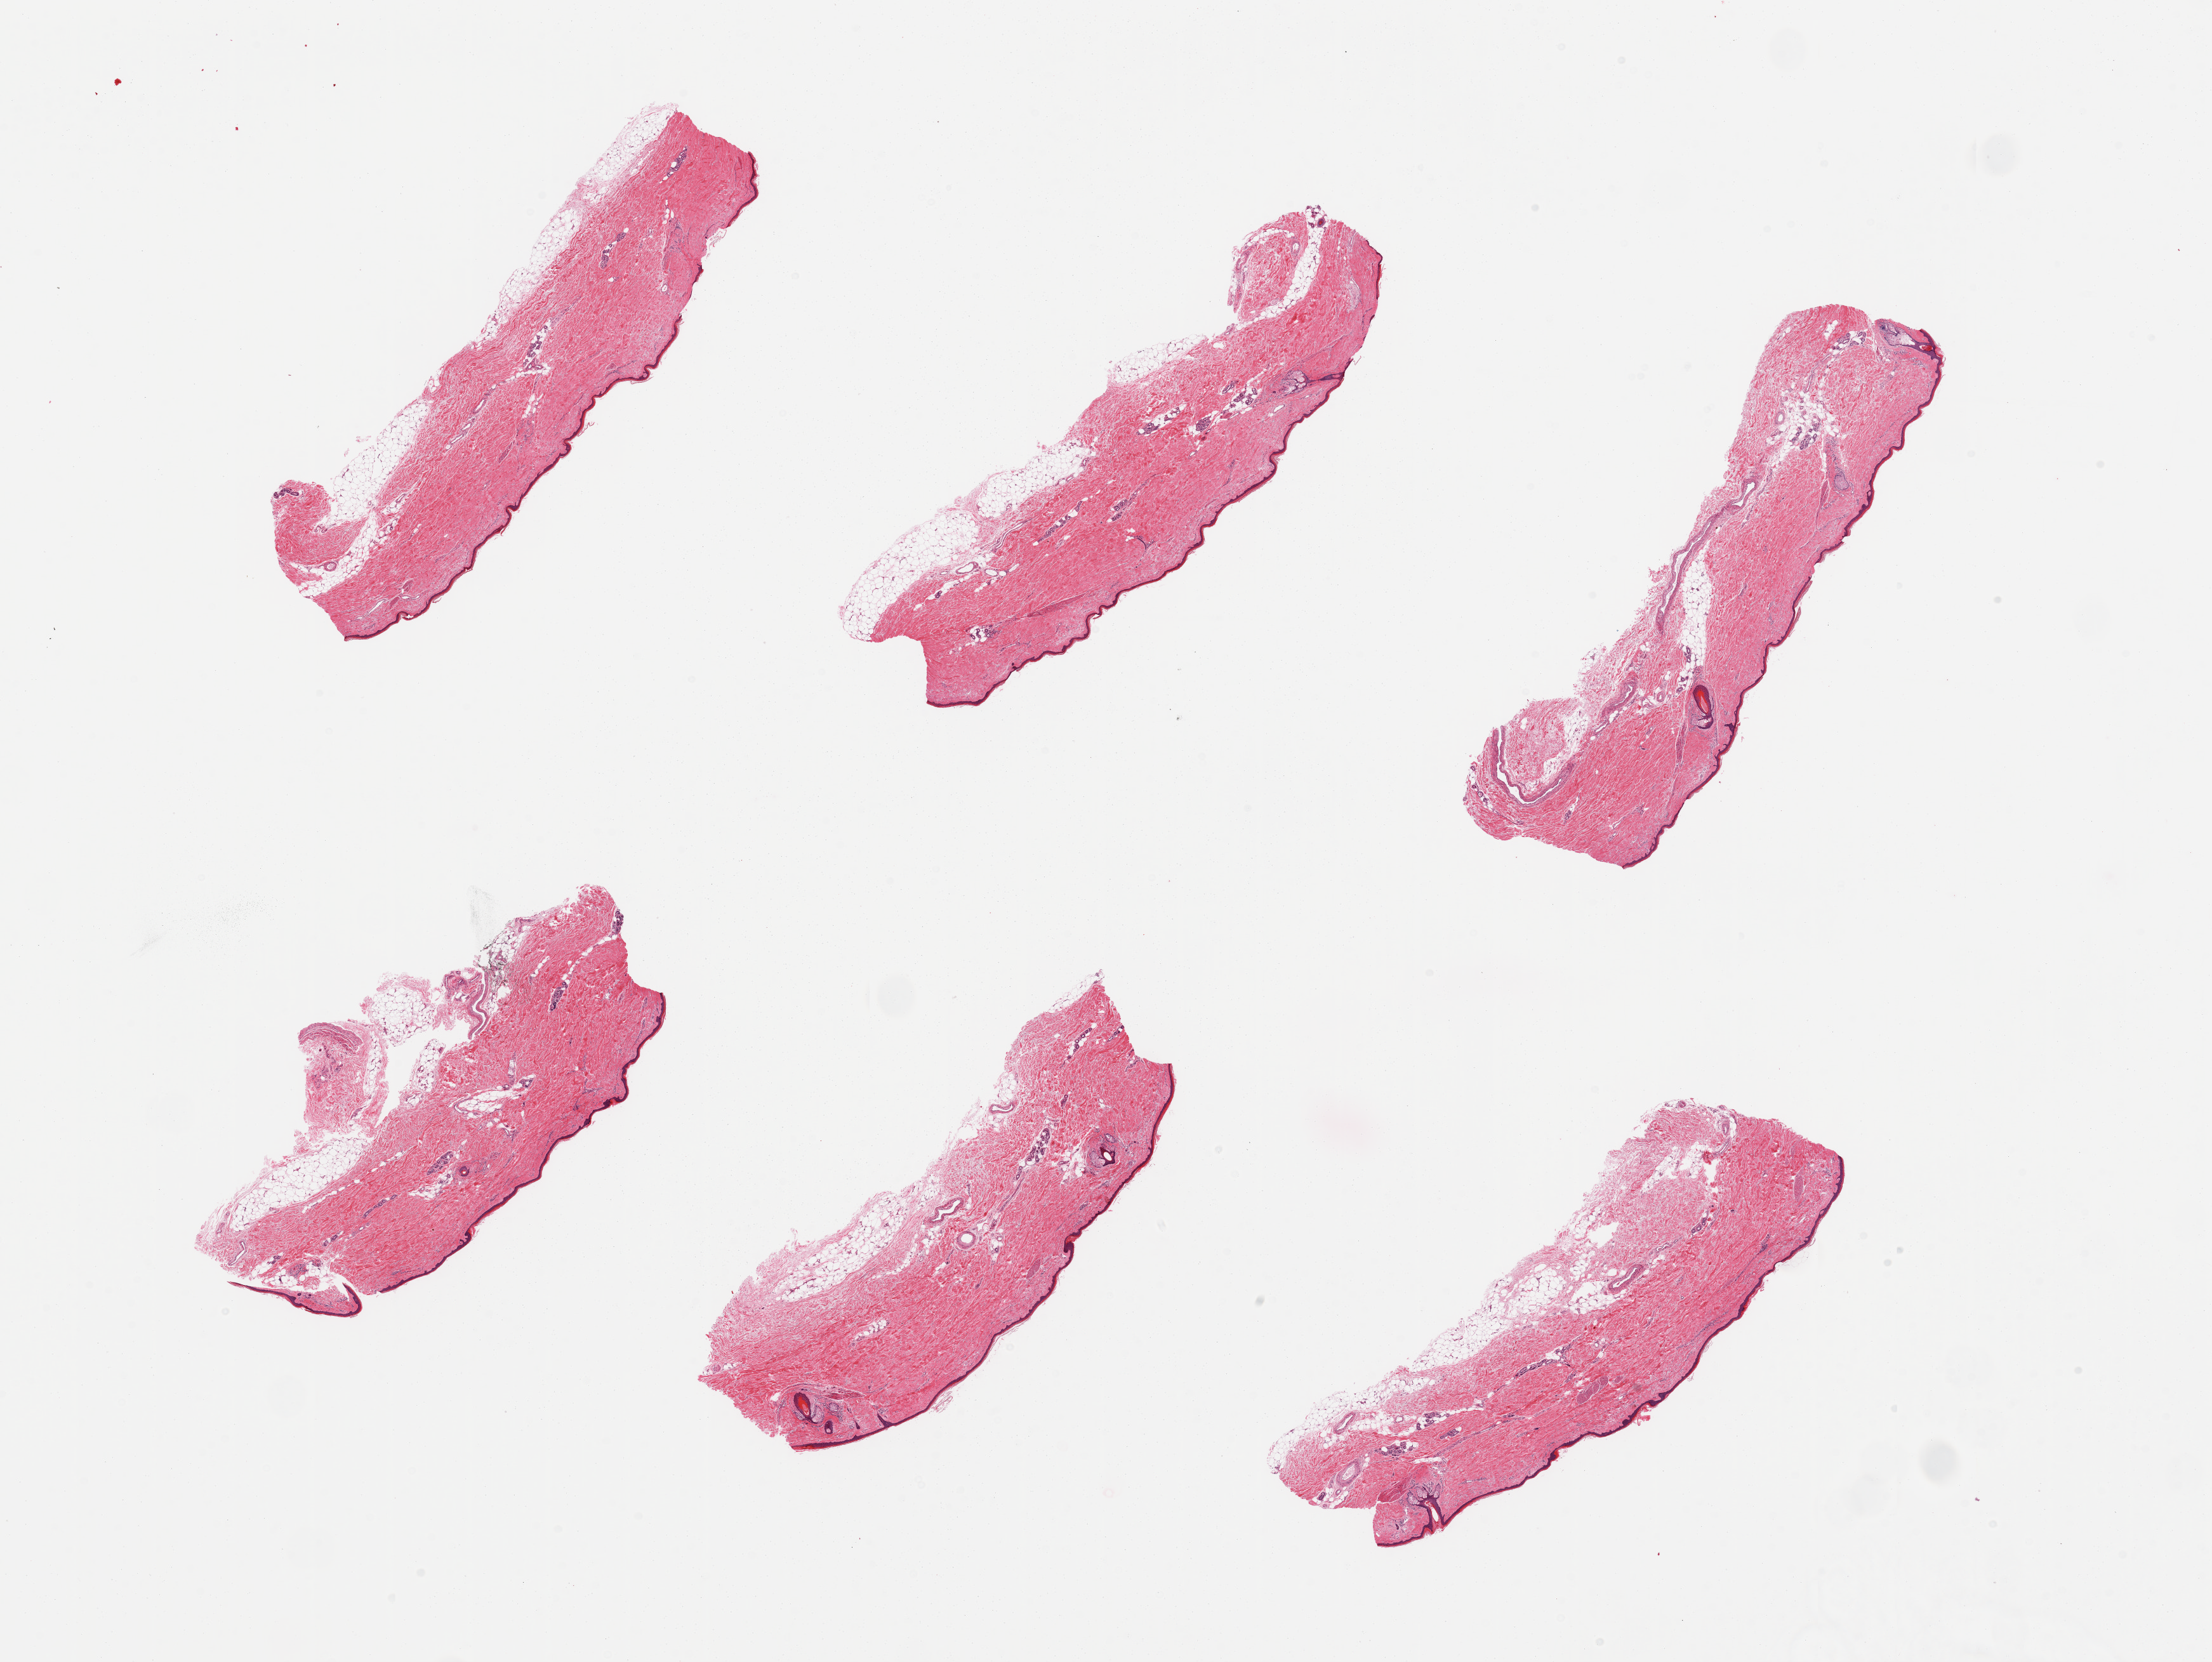
H&E whole-slide image, a low-resolution overview of the entire scanned area, about 27.6 x 20.7 mm; PAXgene-fixed, paraffin-embedded tissue; sampled site (target tissue): skin of lower leg; tissue donor sample. Donor: male.
• review note (as recorded): 6 pieces; up to 0.5mm subcutaneous fat